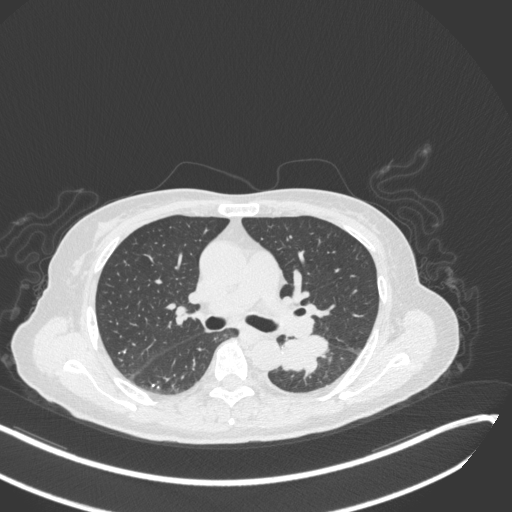
Chest CT, one axial slice. Reconstruction kernel B31f. Lung window (W 1500 / L -600 HU). 1 mm slice thickness. 512 × 512 image matrix. Female patient, age 64 years. From the clinical record (not read from this slice): clinical TNM (as recorded): T3 N1 M1; histopathological grade: G3.
Structures marked on this image (bounding box drawn by a radiologist):
- lung tumour (recorded histology: small cell carcinoma): bounding box <276,331,330,378> (left, top, right, bottom; pixels)